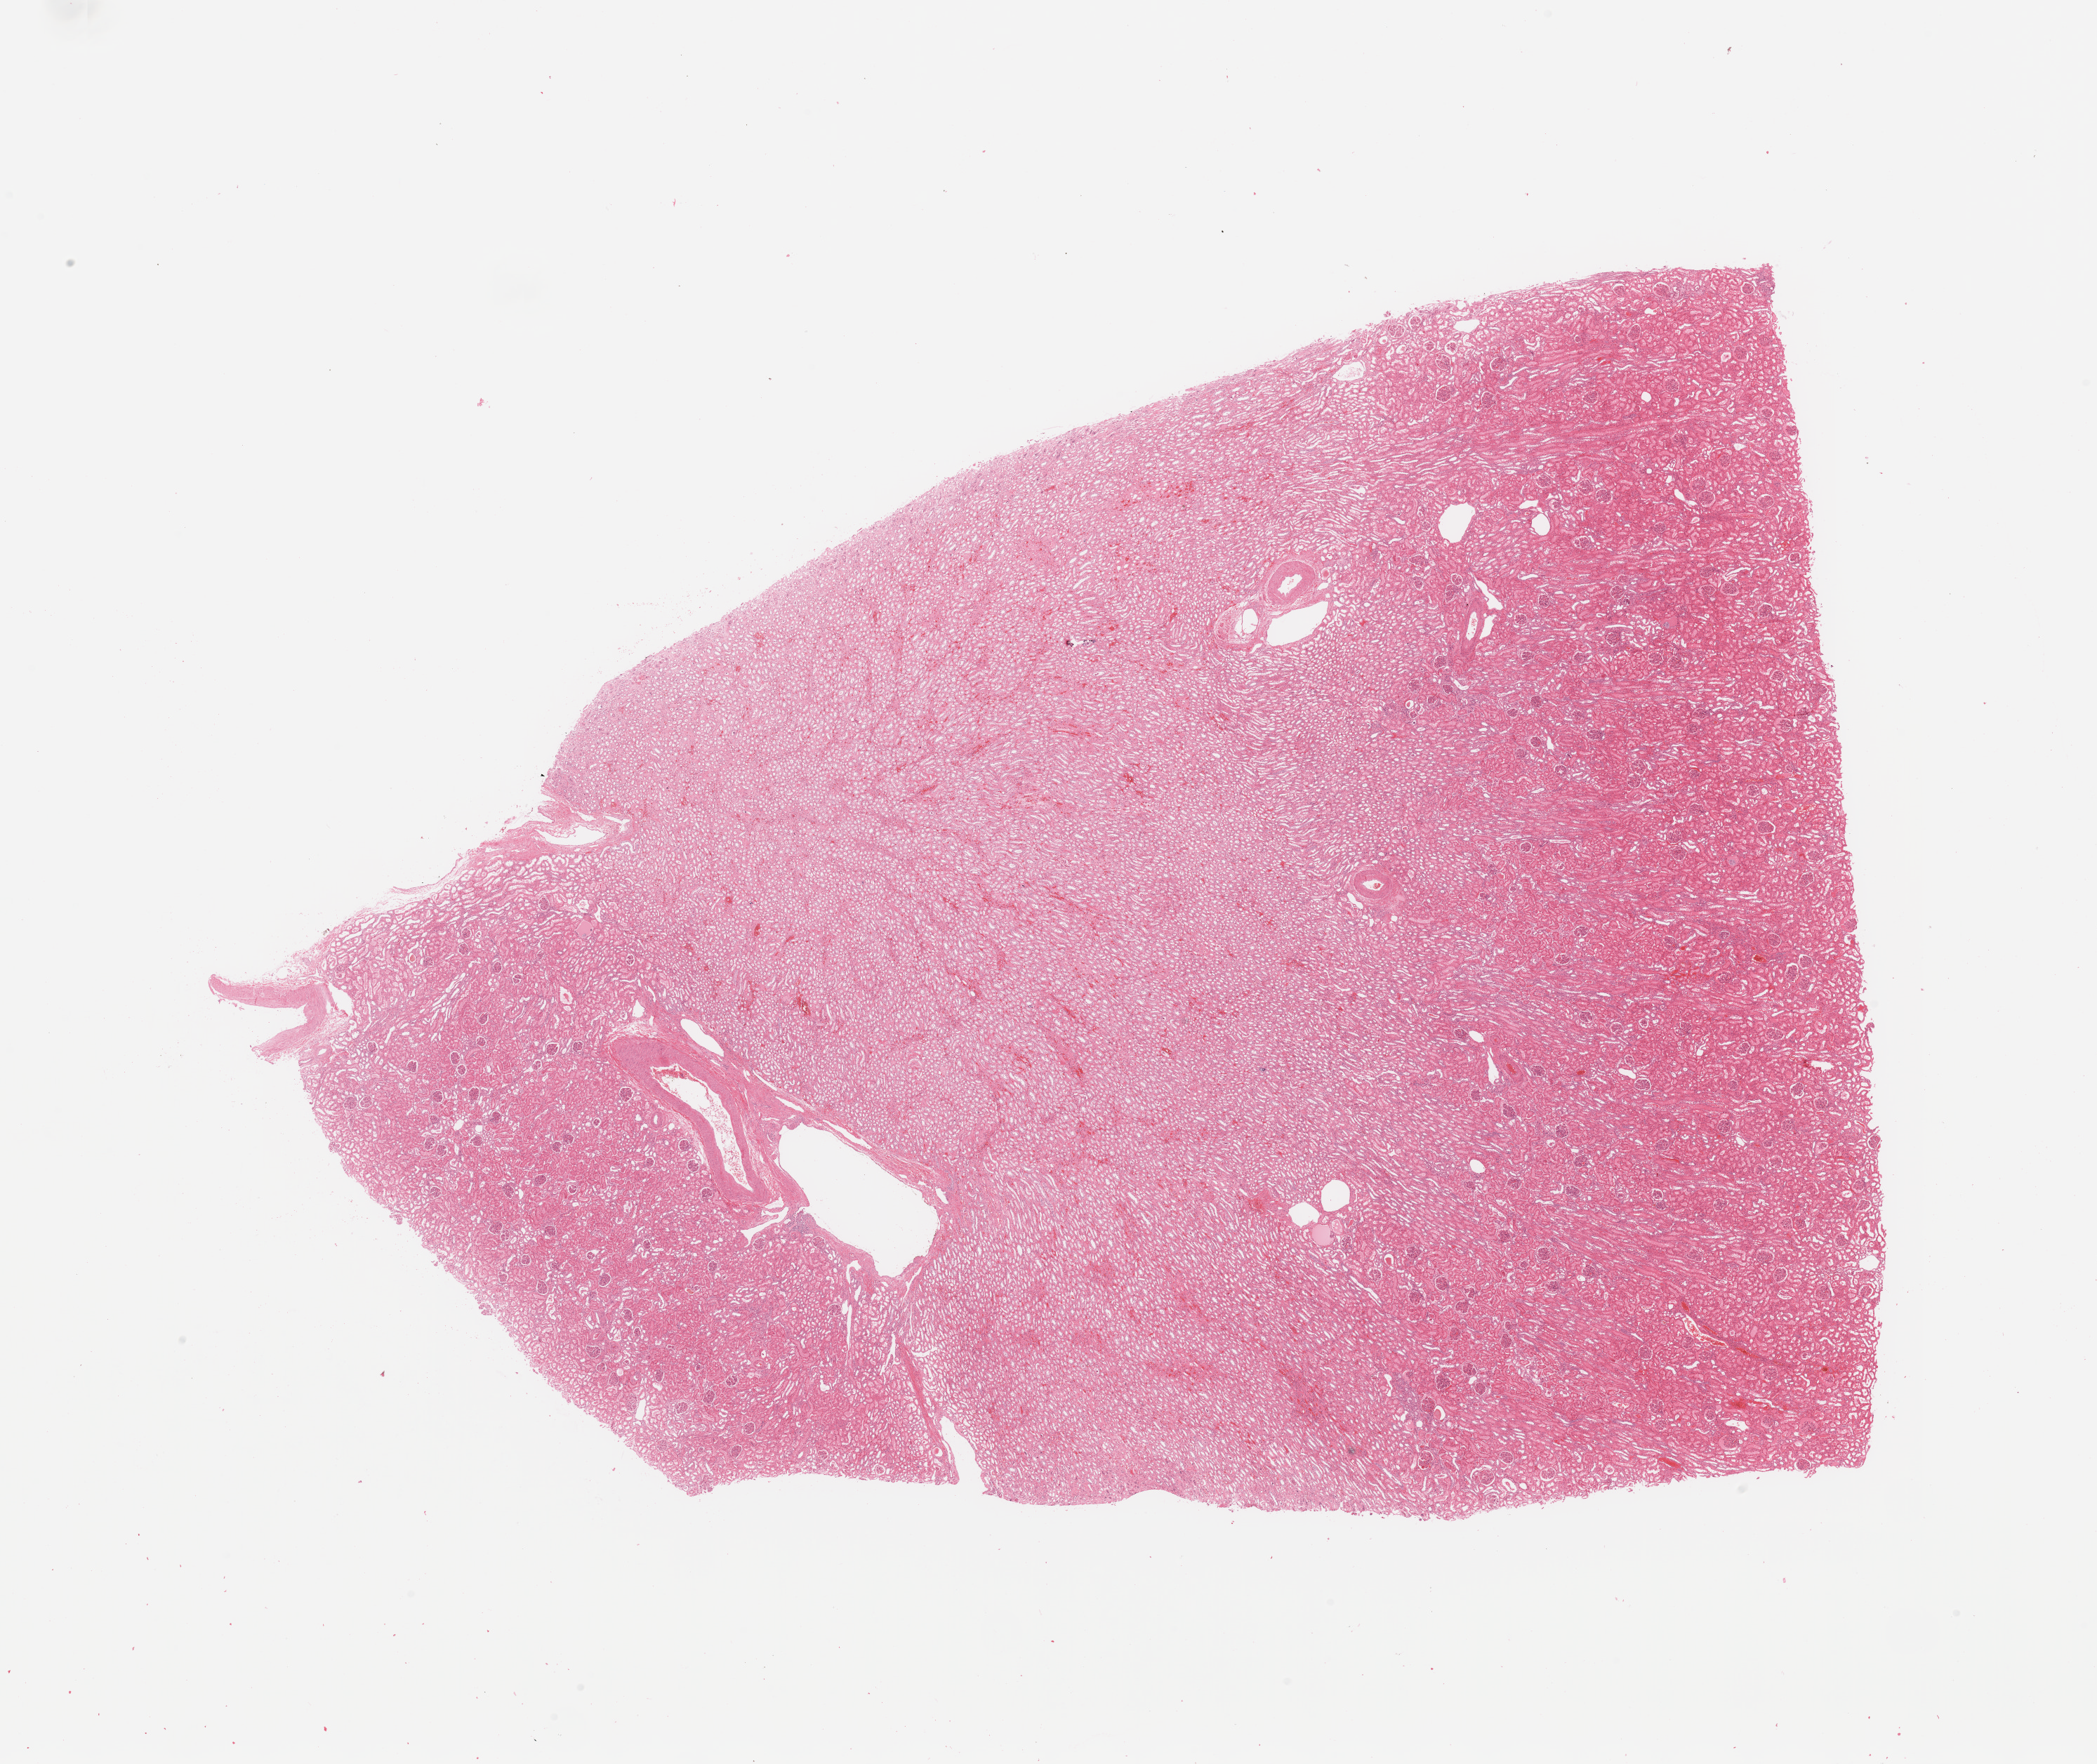
Digitized Hematoxylin and eosin (H&E) stained tissue section (whole slide), shown as a low-resolution overview of the whole scanned area (about 23.6 x 19.9 mm, from a 20x scan); kidney, normal (non-tumour) tissue. 51-year-old male patient.
This section: normal (non-tumour) tissue from the same patient. Patient diagnosis: Renal cell carcinoma, NOS.